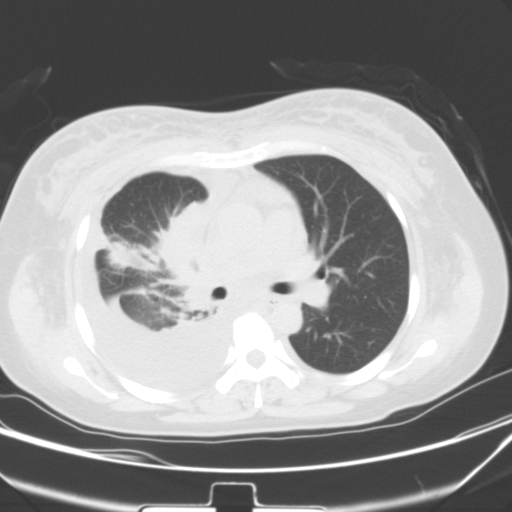
Chest CT, one axial slice; slice 31 of 54 in the series (ordered by position); lung window (W 1500 / L -600 HU); 512 × 512 image matrix, field of view 347 × 347 mm. Female patient, age 36 years. Case-level facts recorded for this patient, not image findings: clinical TNM (as recorded): T1b N2 M0.
Outlined on this slice (bounding box drawn by a radiologist):
- lung tumour (recorded histology: adenocarcinoma): bounding box <157,198,219,317> (left, top, right, bottom; pixels)